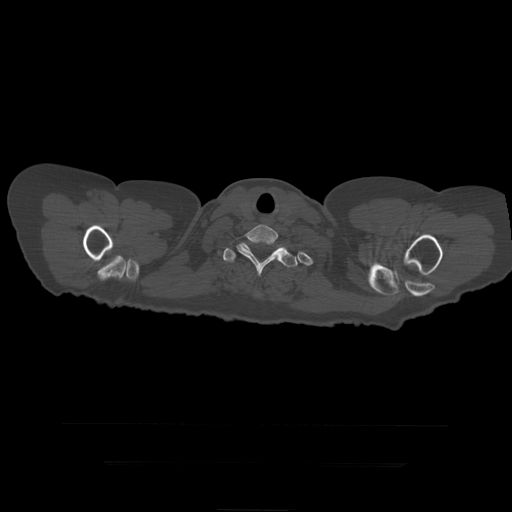
CT including the spine, one axial slice; slice 383 of 399 in the series (ordered by position); reconstruction kernel STANDARD; bone window (W 1800 / L 400 HU); 512 × 512 image matrix, field of view 450 × 450 mm. Patient age 41 years. From the clinical record (not read from this slice): primary cancer: breast.
Annotated regions visible in this slice (semi-automatic segmentation, software-assisted and operator-edited):
- T1 vertebra: bounding box (x1, y1, x2, y2) in pixels: (236, 225, 289, 277)
- T2 vertebra: (223, 241, 298, 268)